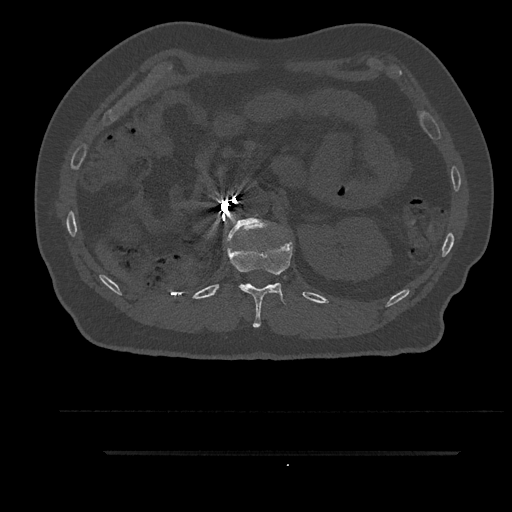
CT including the spine, one axial slice; slice 225 of 797 in the series (ordered by position); 120 kVp; bone window (W 1800 / L 400 HU); 512 × 512 image matrix, field of view 432 × 432 mm. Male patient, age 63 years. Case-level facts recorded for this patient, not image findings: primary cancer: renal; vertebrae with lytic lesions (as recorded): T8.
Structures marked on this image (semi-automatic segmentation, software-assisted and operator-edited):
- L1 vertebra: bounding box (x1, y1, x2, y2) in pixels: (226, 215, 269, 244)
- T12 vertebra: (227, 229, 293, 328)